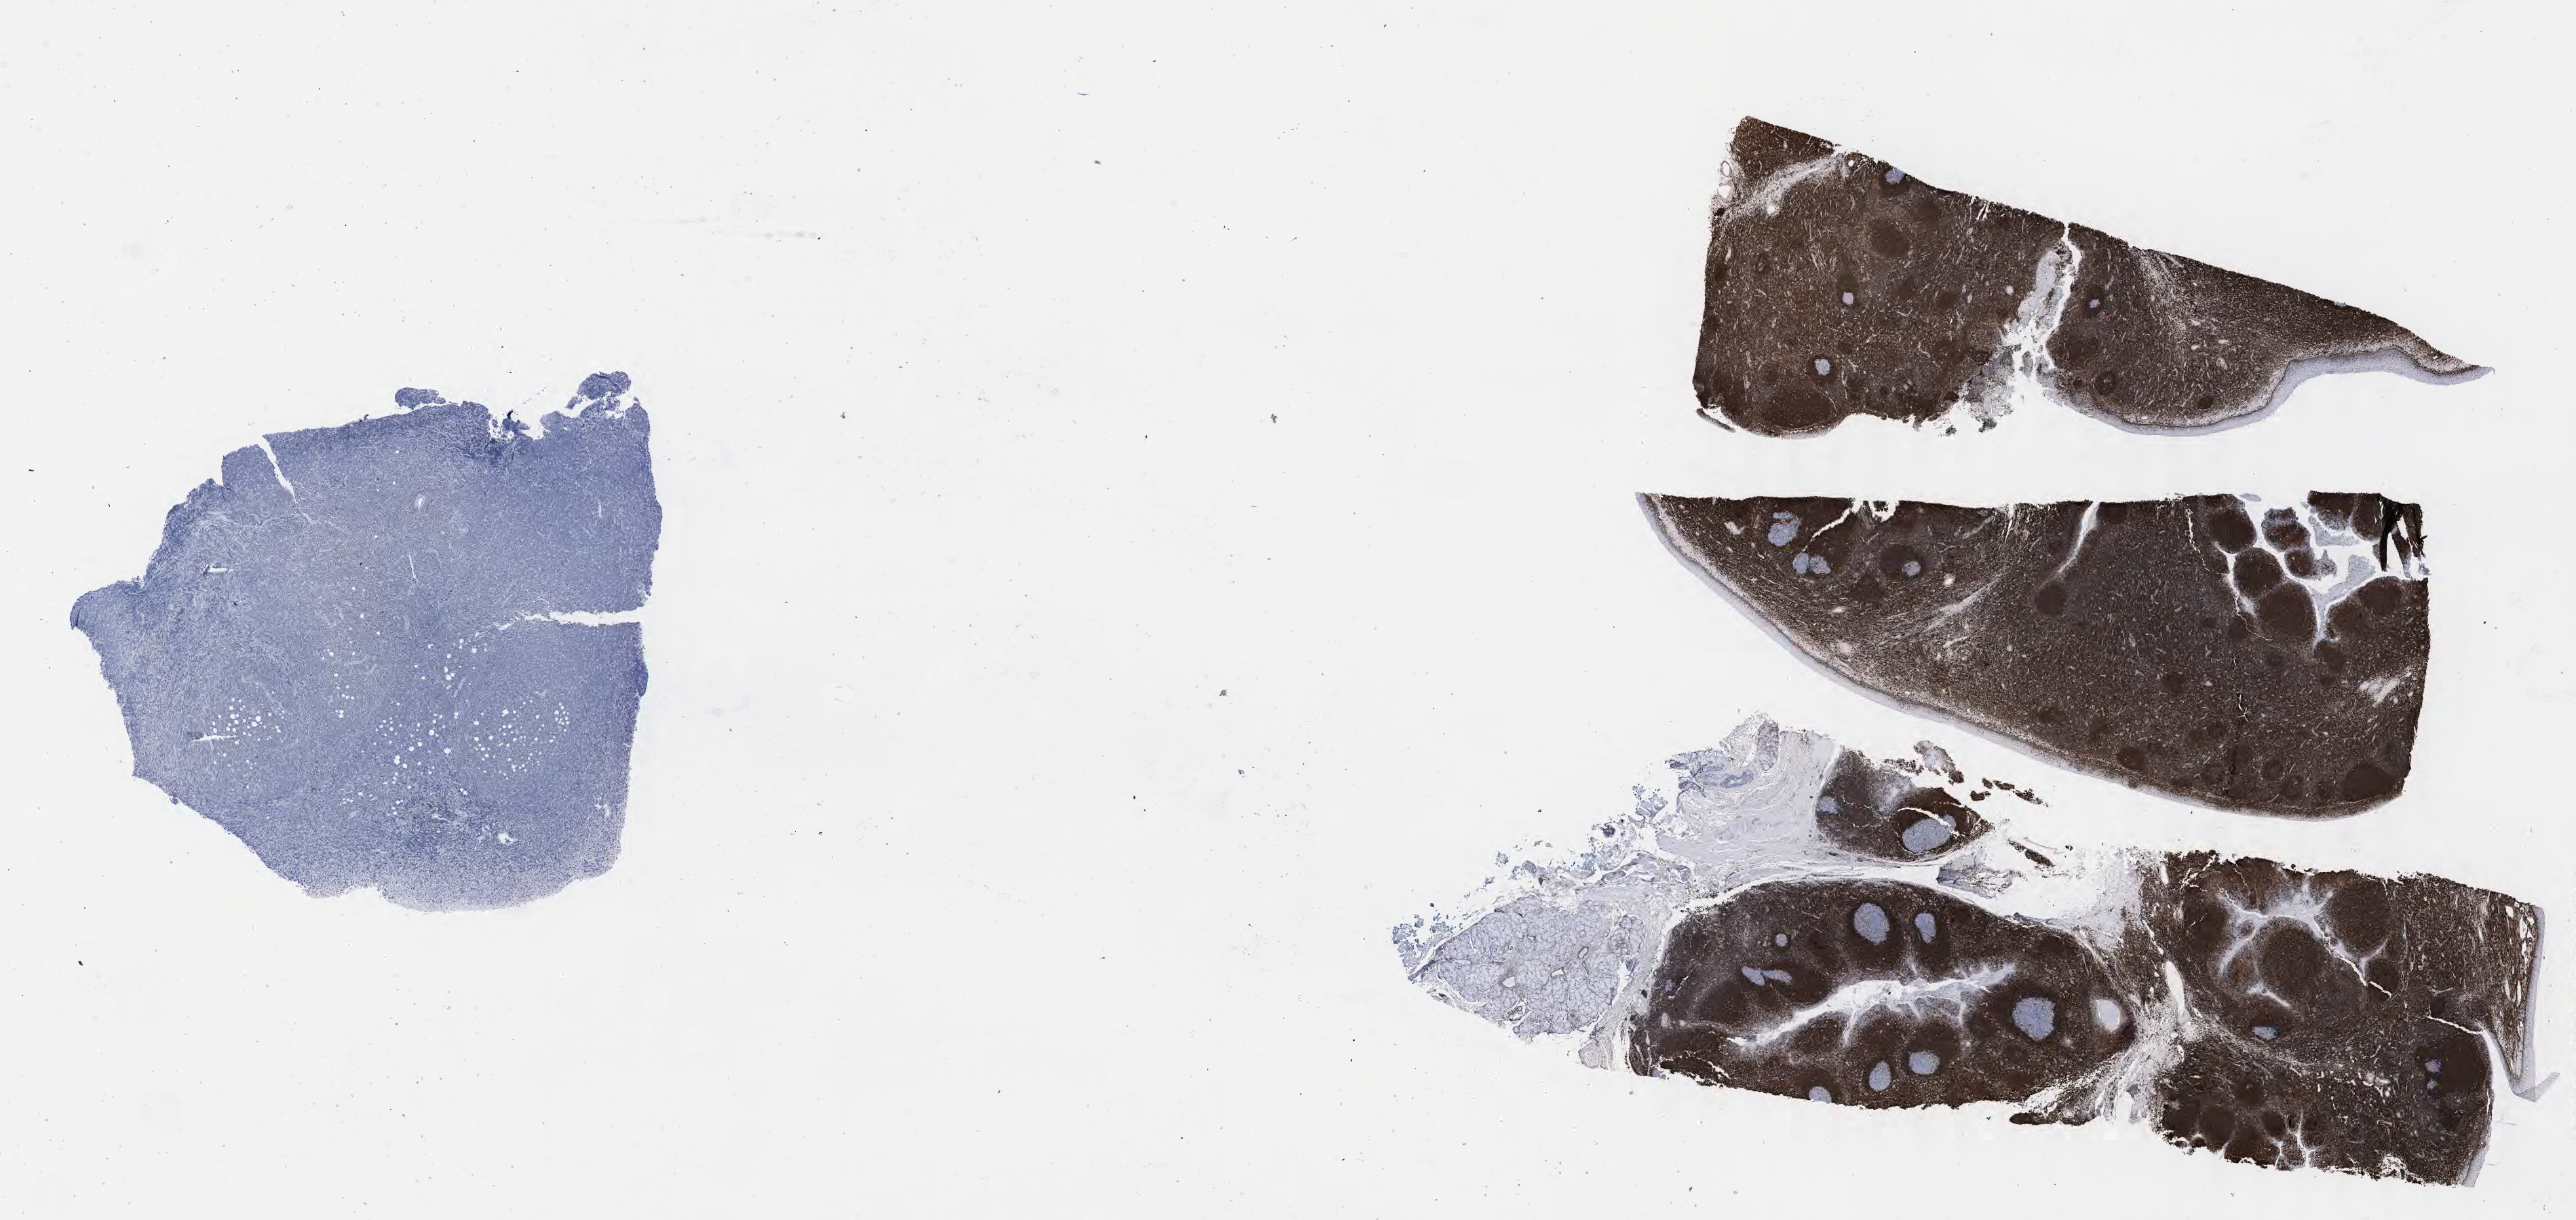
Immunohistochemistry (IHC) whole-slide image stained for BCL2 — shown as a low-resolution overview of the whole scanned area (about 30.7 x 14.5 mm). Tumor tissue. Site: retroperitoneum. Patient: male, age at initial diagnosis 7 years.
Diagnosis: Diffuse large B-cell lymphoma, NOS.